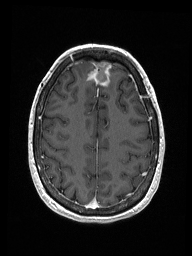
Brain MRI from a brain-tumour surgery series, one axial slice. T1-weighted post-contrast. 1 mm slice thickness. 192 × 256 image matrix. Case-level facts recorded for this patient, not image findings: histopathology: Metastastic Carcinoma from Breast primary; tumour location: Right Frontal.
Outlined on this slice (manually delineated by an expert):
- previous resection cavity: bounding box [x1, y1, x2, y2] px = [93, 61, 112, 85]